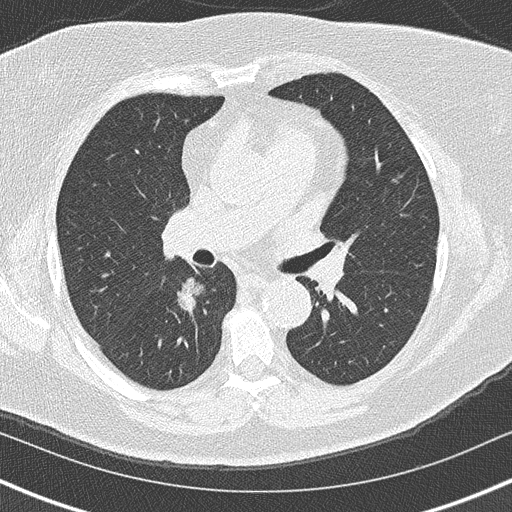
Chest CT (low-dose screening protocol), one axial image. Second screening round (one year after baseline). Lung window (W 1500 / L -600 HU). 2 mm slice thickness. Female, age 60 years at enrolment.
• Lesion marked by an expert reader, bounding box (x1, y1, x2, y2) in pixels: (150, 266, 215, 323).
• The exam's reader record, not a measurement of the box and not confirmed to be the same lesion: non-calcified nodule or mass ≥4 mm, right lower lobe, 20 × 19 mm, soft tissue attenuation, pre-existing on the prior screen: yes; interval growth: yes.
• Official screen result: positive, other.